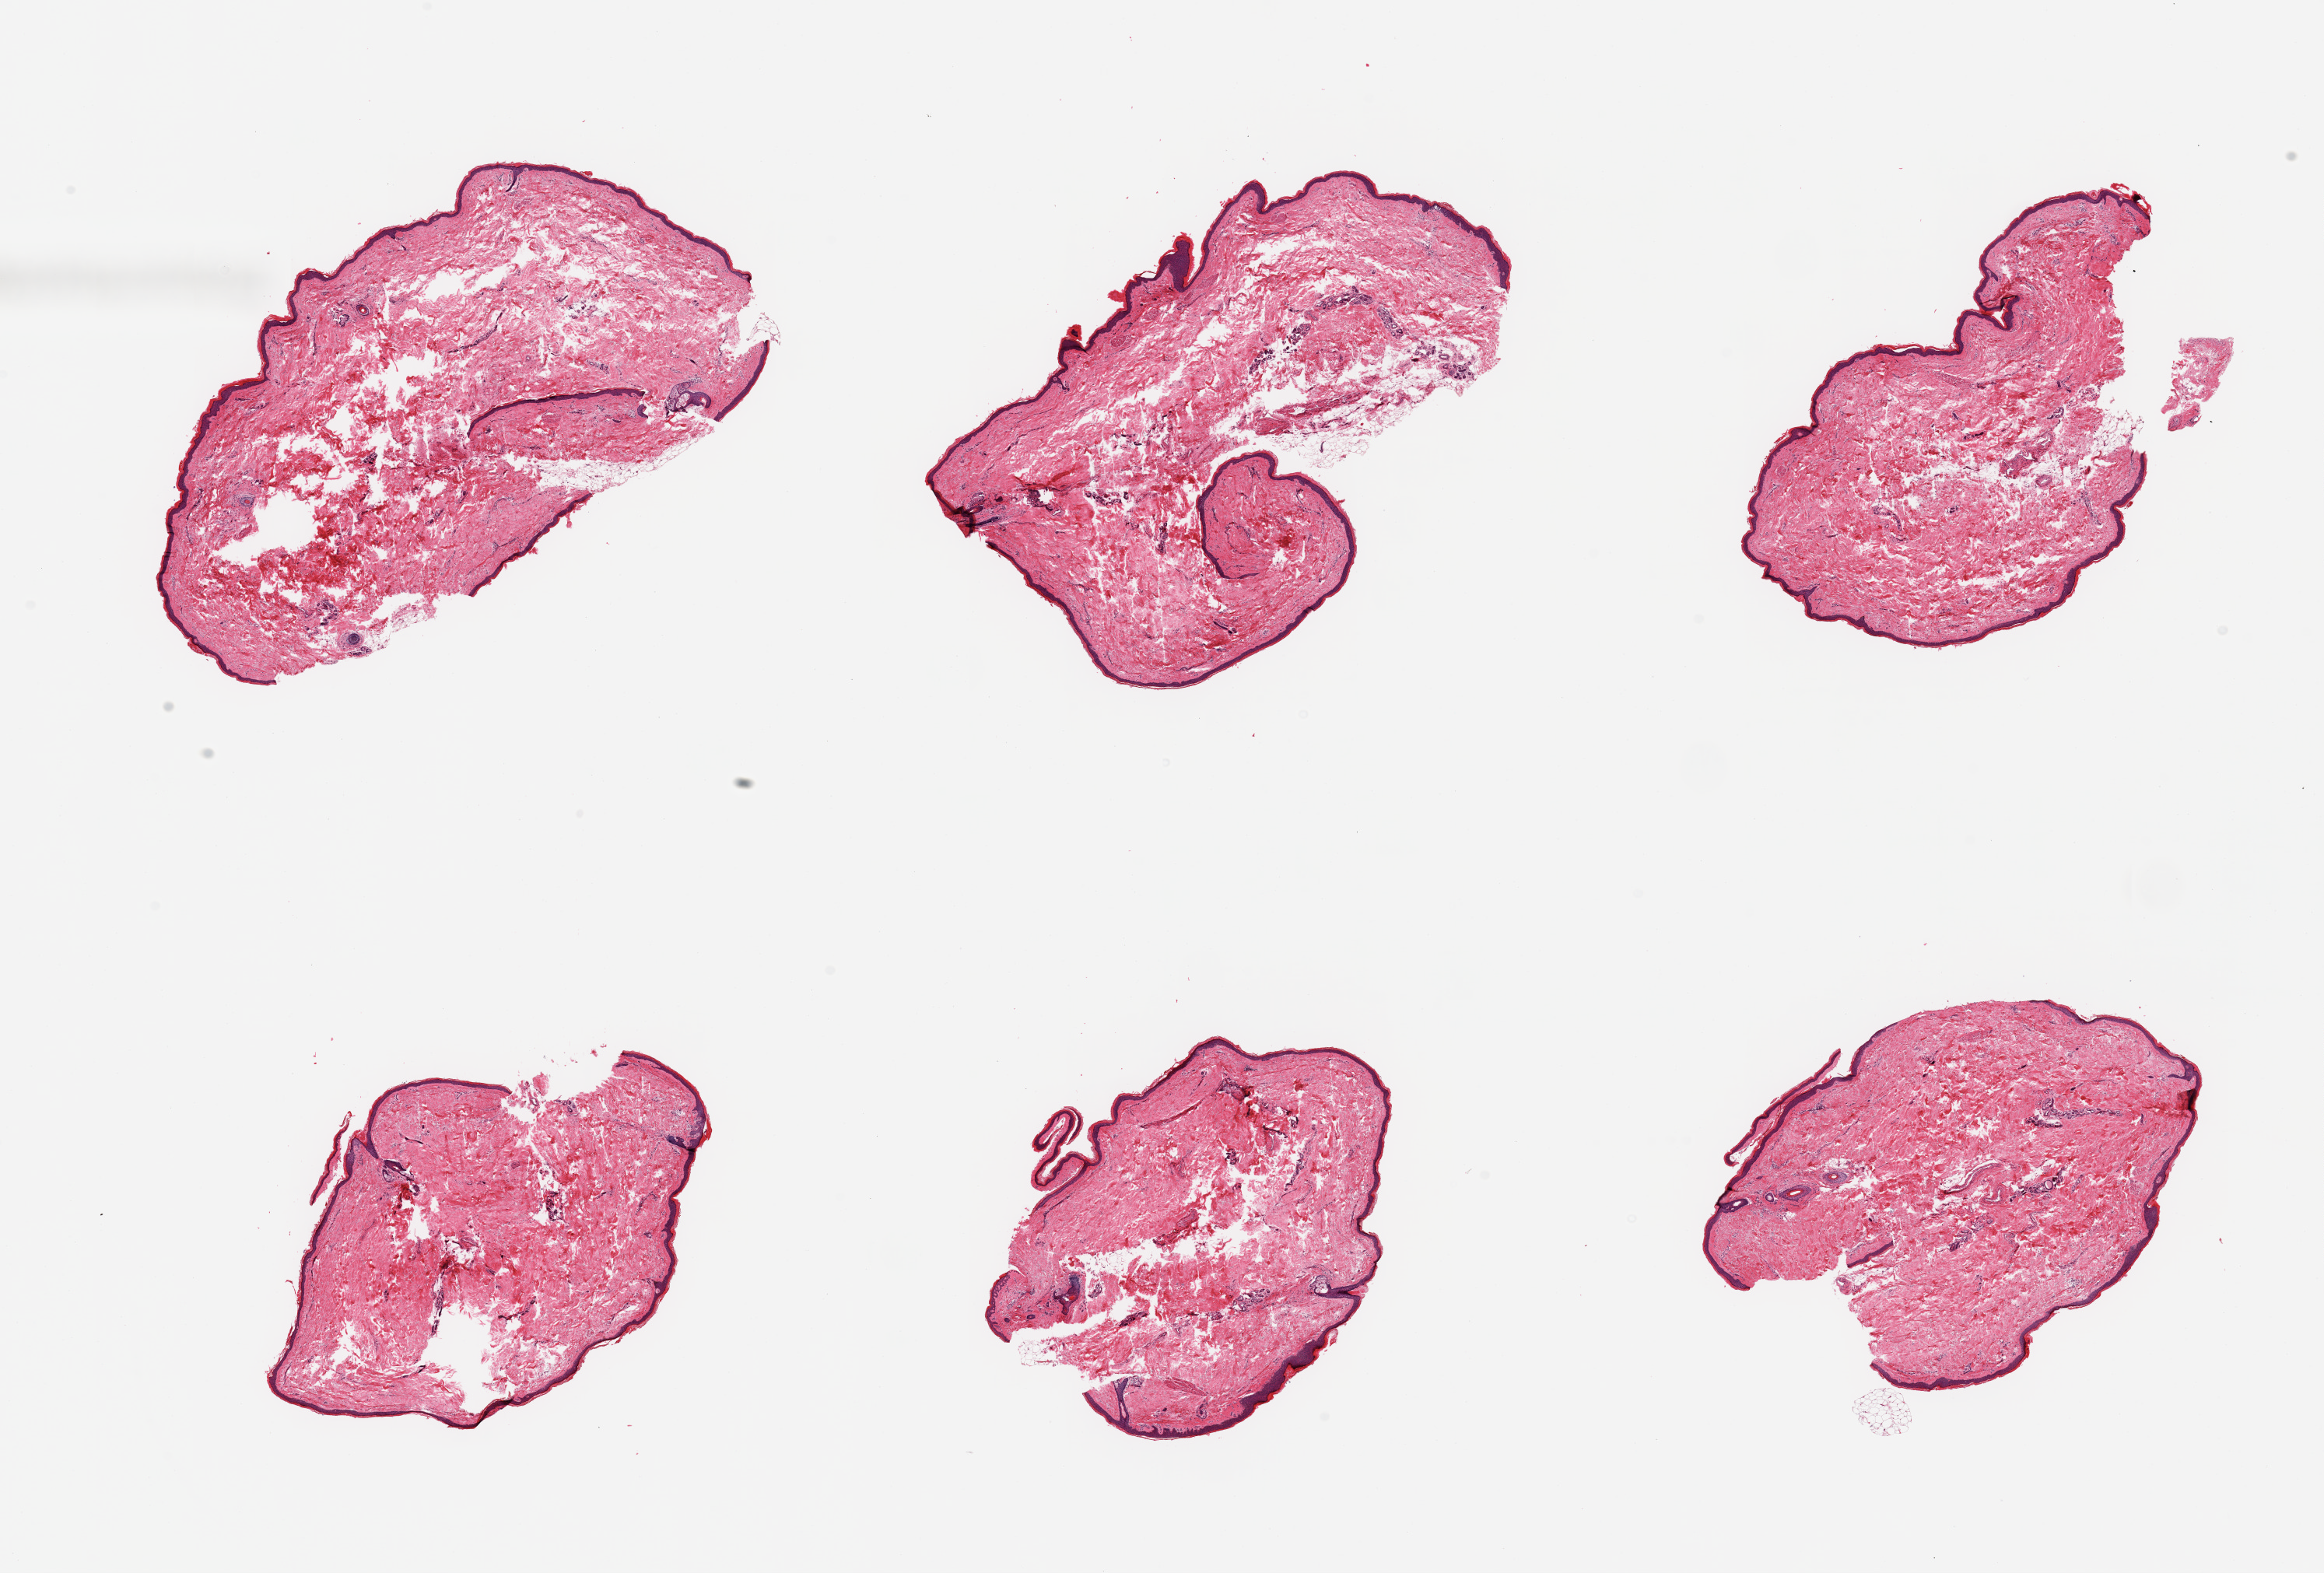
Hematoxylin and eosin (H&E) whole-slide image, brightfield — whole scanned area (about 23.6 x 16.0 mm, acquisition: 20x scan) shown as a low-resolution overview. PAXgene-fixed paraffin-embedded (PFPE) section. Target tissue: skin of lower leg. Tissue donor sample. Donor: male.
- review note (as recorded): 6 pieces, squamous epithelium is ~30-40 microns; minimal adherent dermal fat